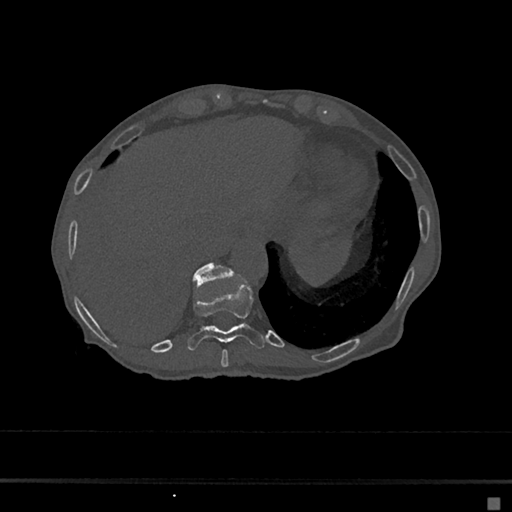
CT including the spine, one axial slice; slice 222 of 797 in the series (ordered by position); reconstruction kernel Br40s/3; bone window (W 1800 / L 400 HU); 0.5 mm slice thickness; 512 × 512 image matrix, field of view 360 × 360 mm. Female patient, age 68 years. Case-level facts recorded for this patient, not image findings: primary cancer: renal.
Outlined on this slice (semi-automatic segmentation, software-assisted and operator-edited):
- T10 vertebra: box from (x=188, y=282) to (x=265, y=351) px
- T11 vertebra: (x=192, y=263)–(x=233, y=287)
- T9 vertebra: (x=221, y=349)–(x=229, y=367)